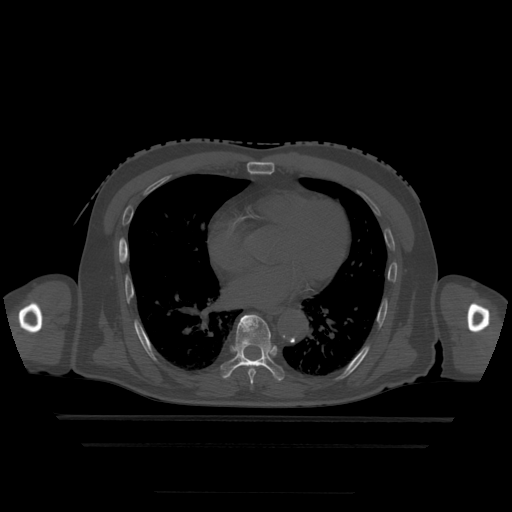
CT including the spine, one axial slice; slice 285 of 522 in the series (ordered by position); bone window (W 1800 / L 400 HU); 1.25 mm slice thickness; 512 × 512 image matrix. Patient age 68 years. From the clinical record (not read from this slice): primary cancer: urothelial.
Annotated regions visible in this slice (semi-automatically segmented with operator editing):
- T6 vertebra: box from (x=251, y=384) to (x=253, y=389) px
- T7 vertebra: (x=248, y=369)–(x=256, y=384)
- T8 vertebra: (x=221, y=315)–(x=285, y=382)